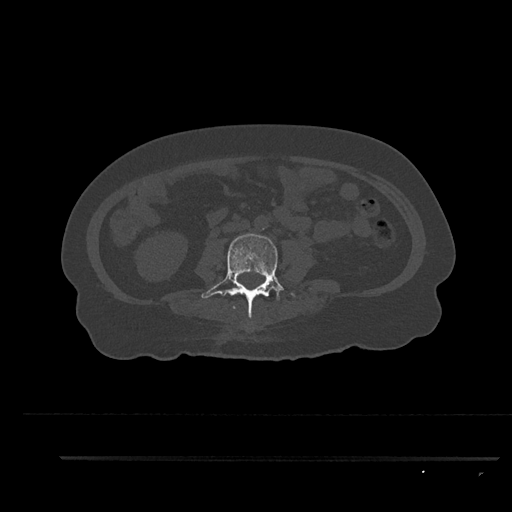
CT including the spine, one axial slice. Position 88 of 797 along the scan axis. 120 kVp. Bone window (W 1800 / L 400 HU). 0.5 mm slice thickness. 512 × 512 image matrix. Female patient, age 44 years. Case-level facts recorded for this patient, not image findings: primary cancer: renal; vertebrae with lytic lesions (as recorded): L1.
Annotated regions visible in this slice (semi-automatic segmentation, software-assisted and operator-edited):
- L3 vertebra: bounding box [x1, y1, x2, y2] px = [201, 233, 295, 319]